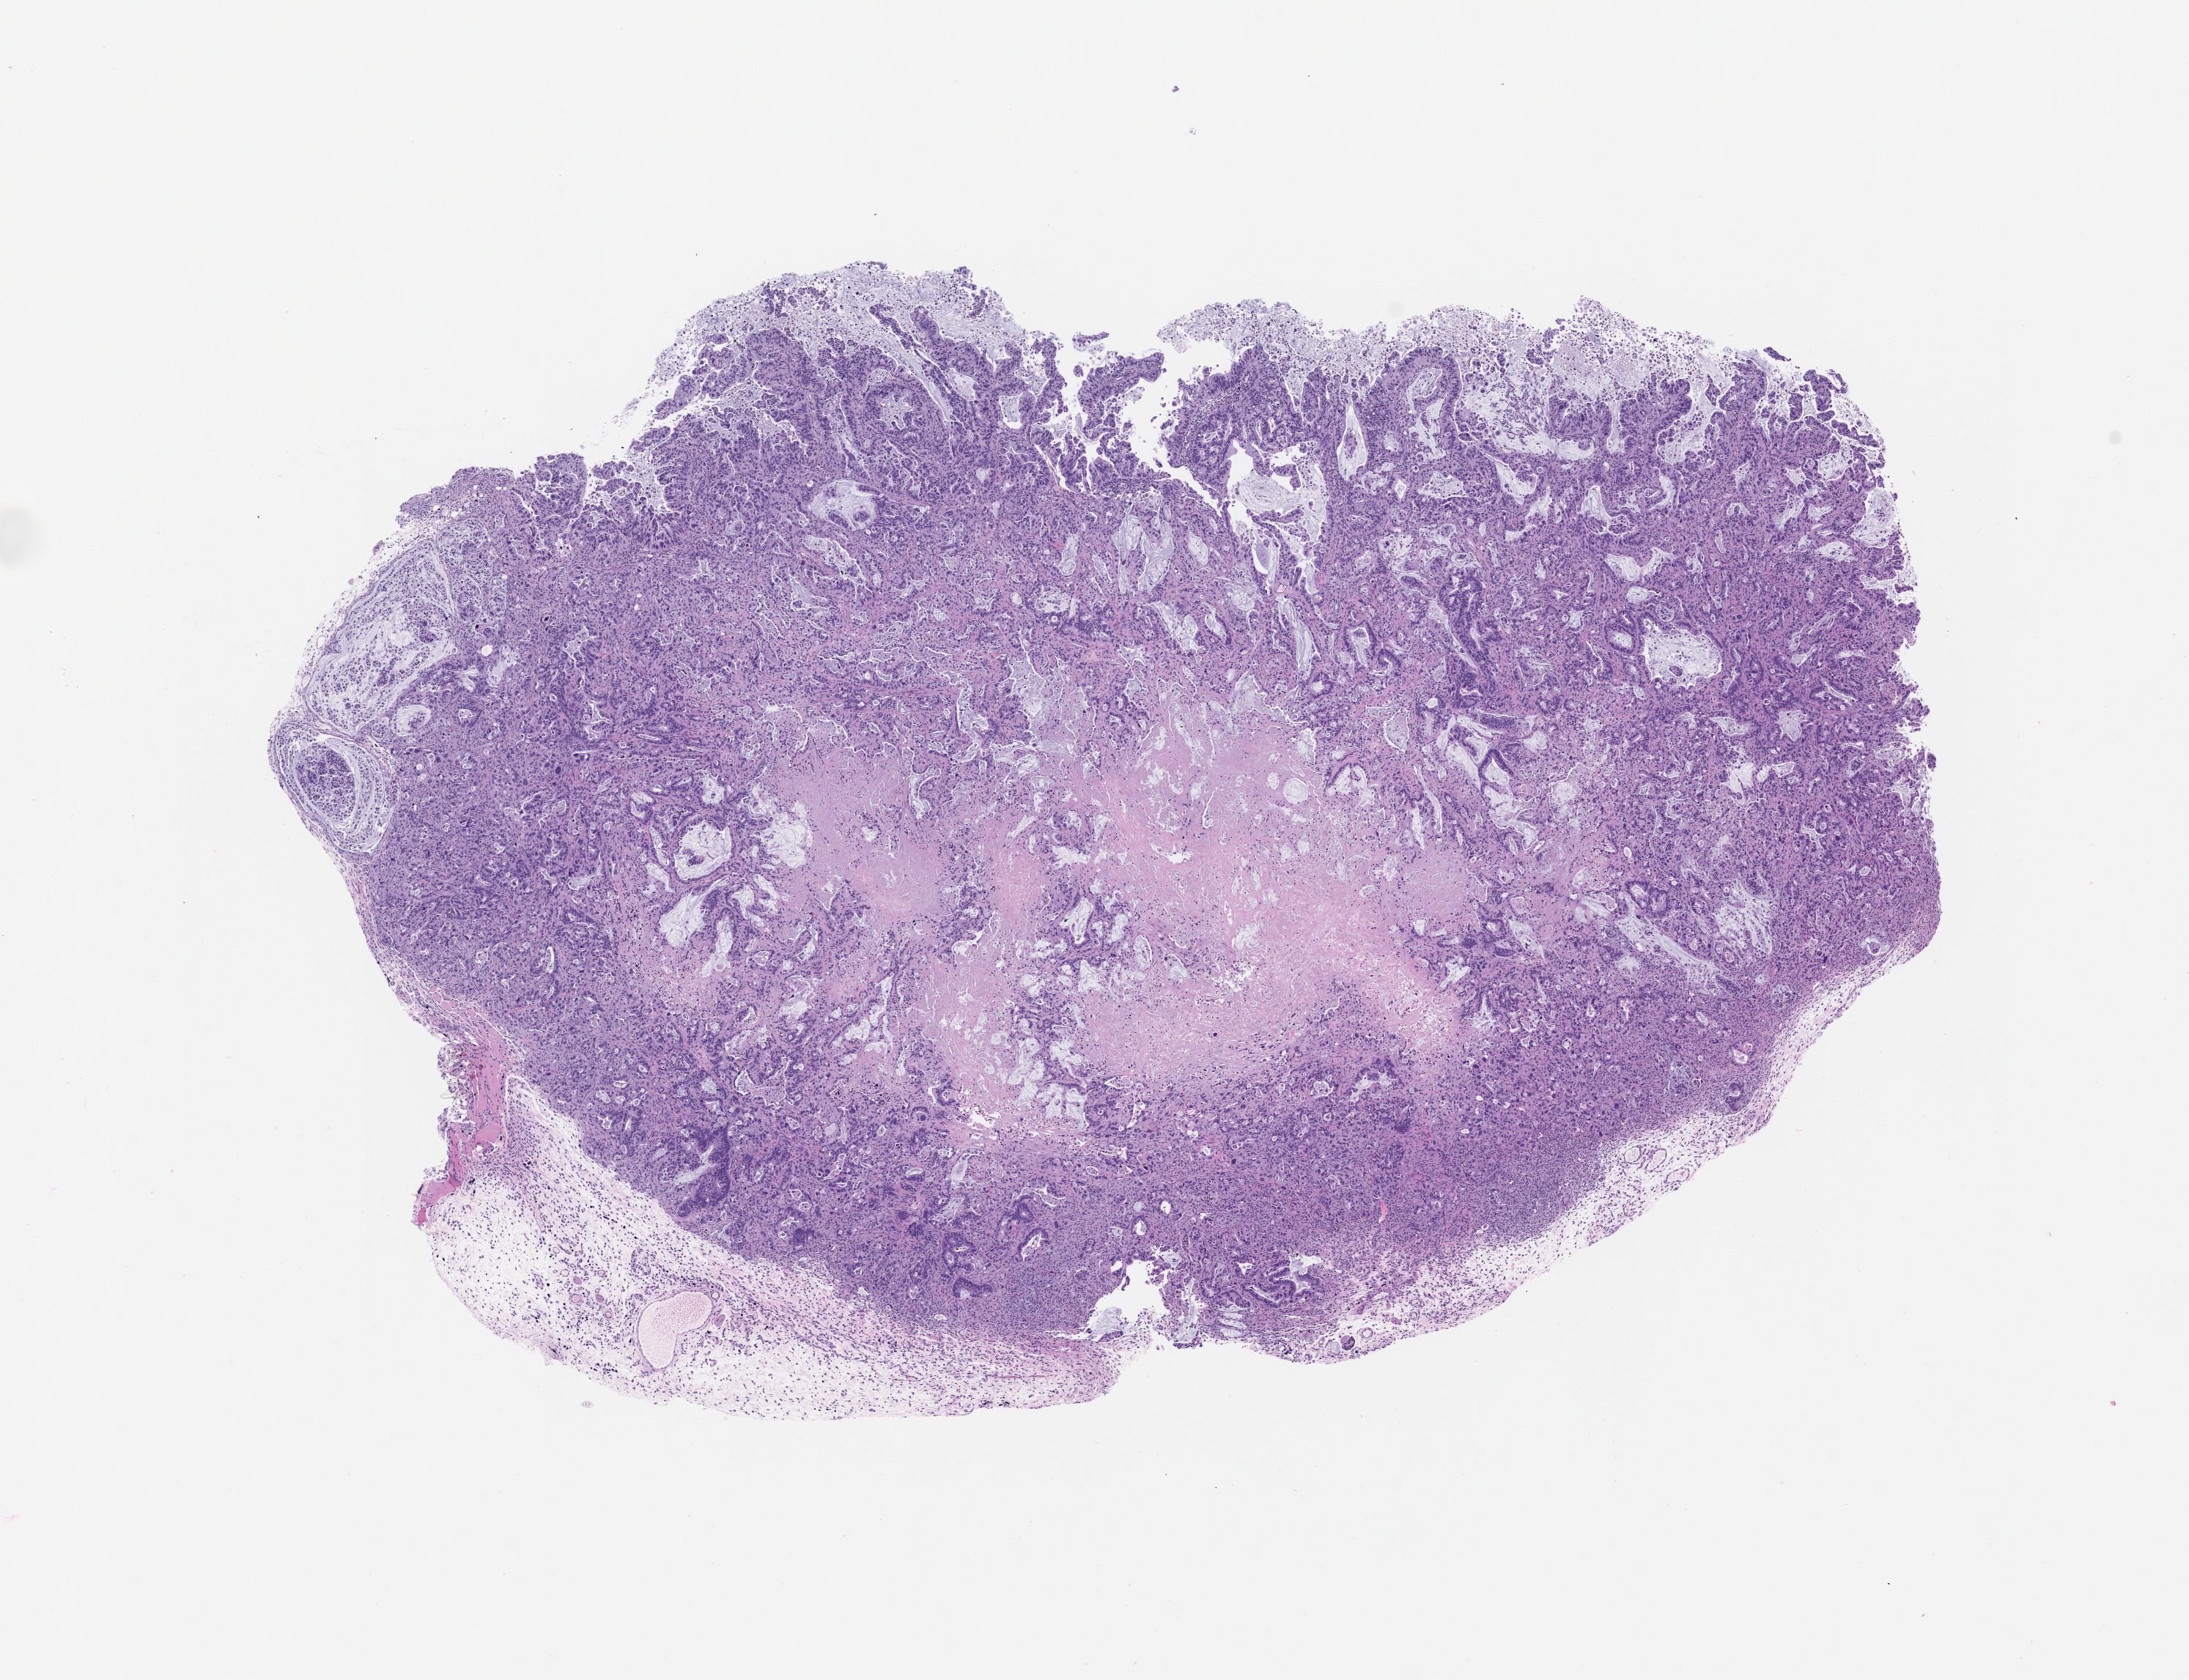
Whole-slide image, H&E: patient-derived xenograft (human tumor grown in a mouse), passage 1 — low-resolution overview of the scanned area, about 12.0 x 9.2 mm, formalin-fixed, paraffin-embedded (FFPE) tissue, tumor site category: pancreas.
* originating patient diagnosis: Pancreatic Adenocarcinoma